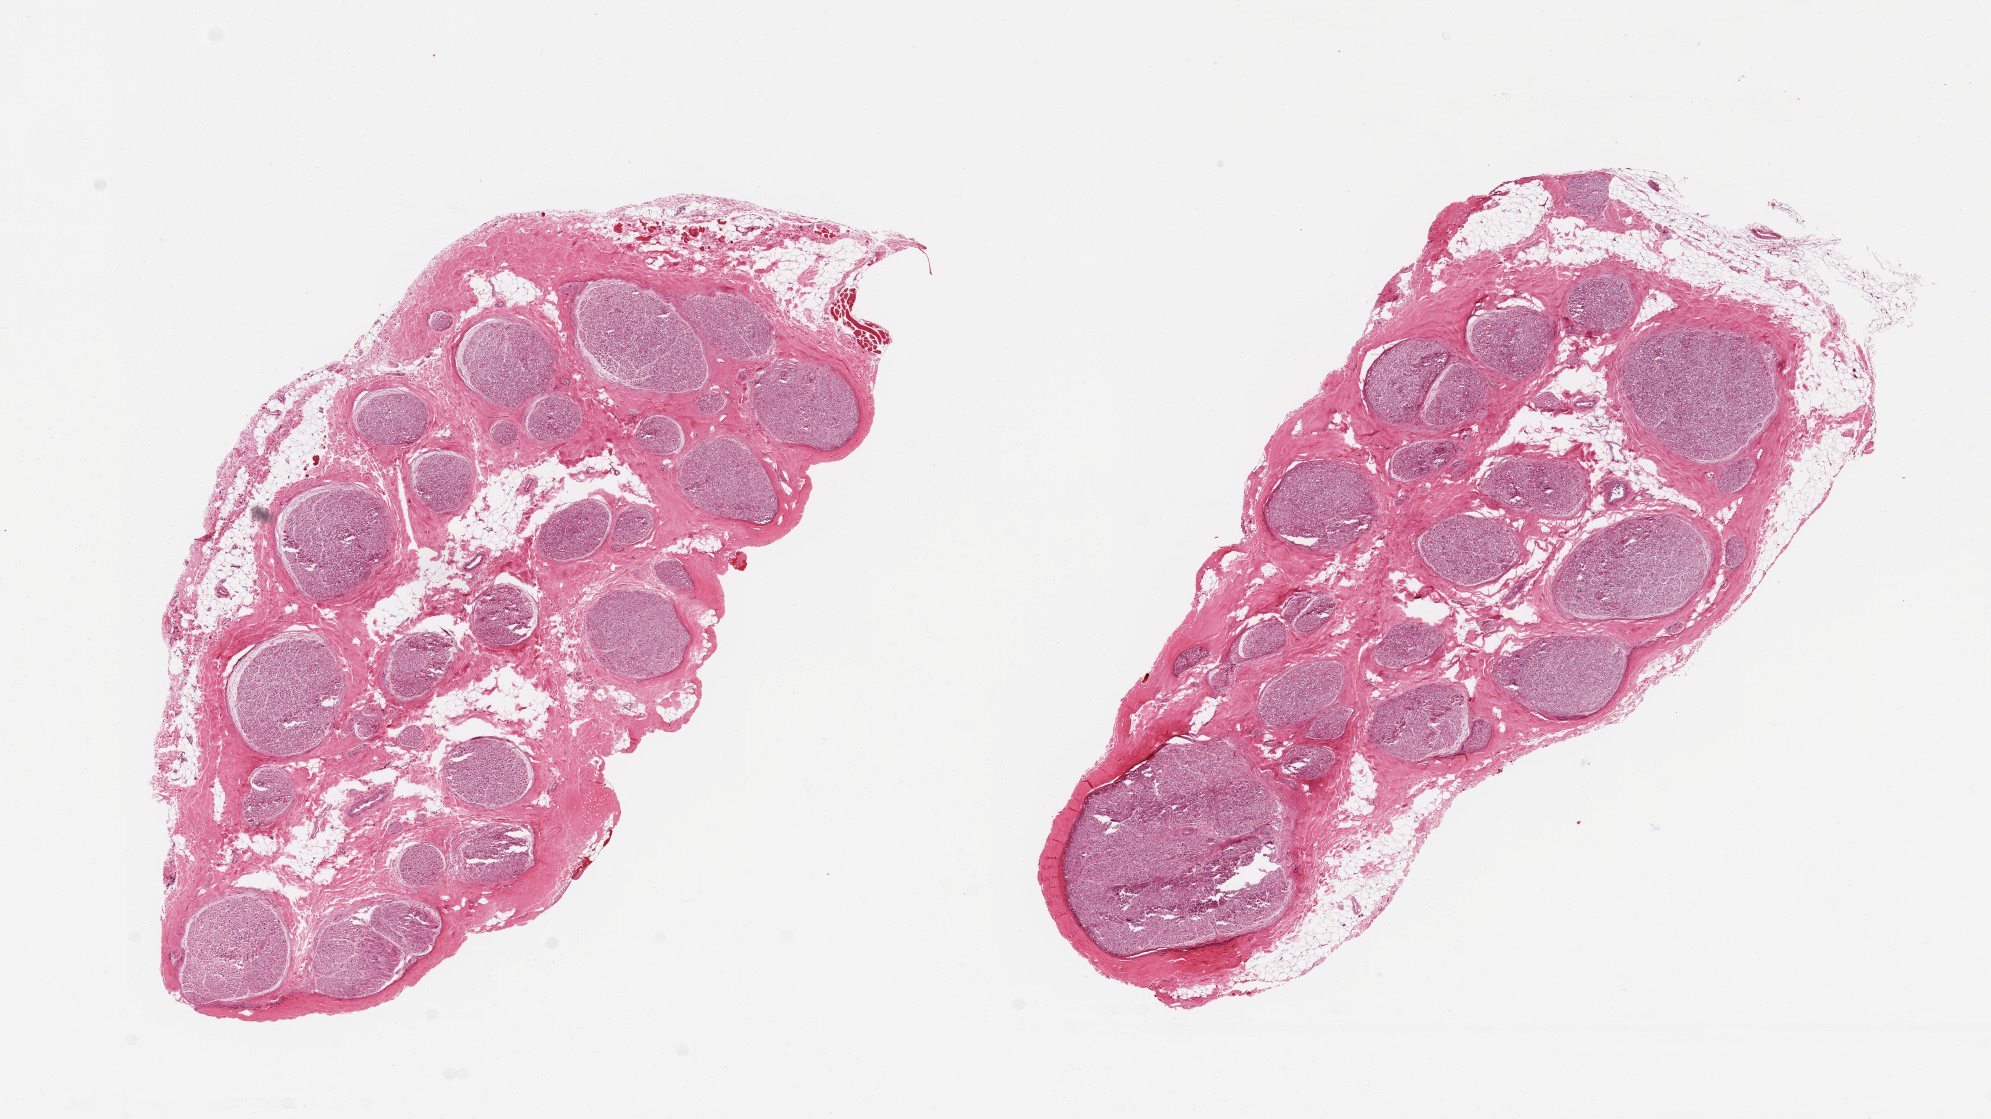
Hematoxylin and eosin (H&E) whole-slide image, brightfield, shown as a low-resolution overview of the whole scanned area (about 15.8 x 8.9 mm); PAXgene-fixed paraffin-embedded (PFPE) section; section of tibial nerve (target tissue); donor tissue sample. Male donor.
Reviewer comment on this tissue sample: 2 ~7x4mm aliquots, fairly clean.